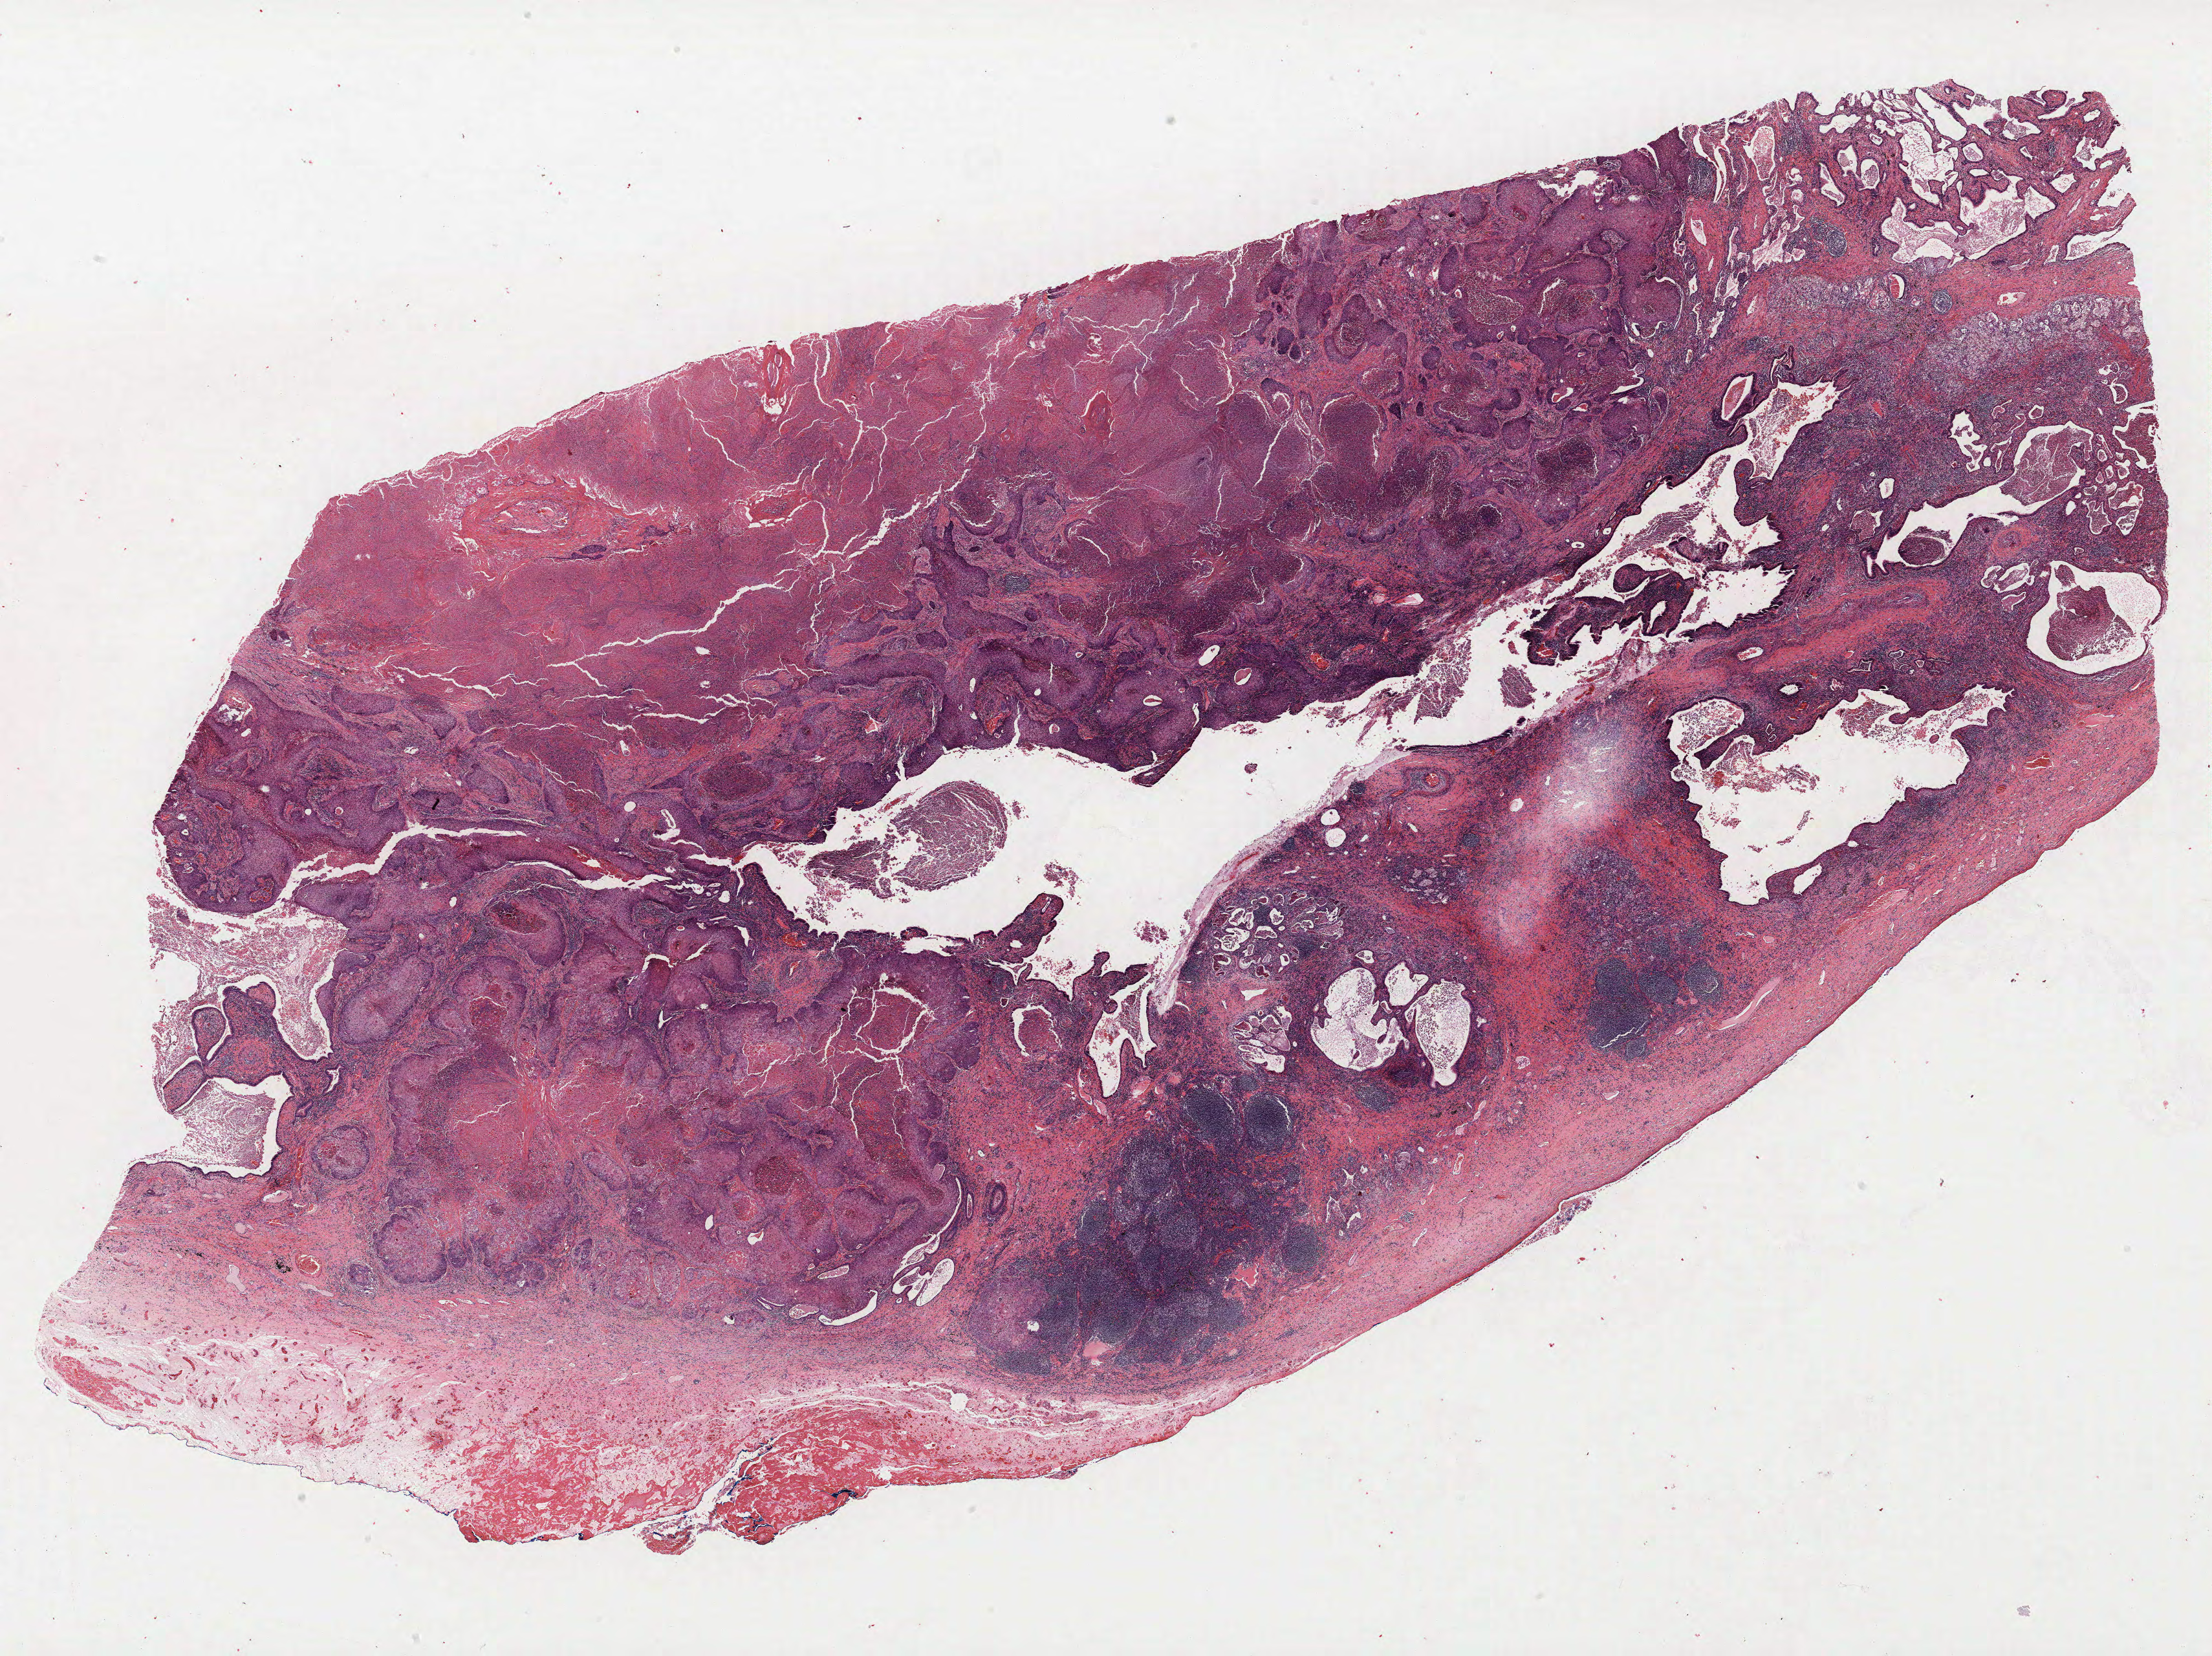
H&E-stained whole-slide image — low-resolution overview of the scanned area, about 27.4 x 20.5 mm (acquisition: 40x scan); FFPE section; lung. Male, age 58 at enrolment. Grade: moderately differentiated (G2).
- primary tumour location (clinical record): right lower lobe
- tumour size (pathology): 38 mm
- stage (AJCC 6th edition): IB
- participant's lung-cancer diagnosis: Squamous cell carcinoma, keratinizing, NOS
- note: participant had 2 primary lung cancers recorded; fields above describe the first